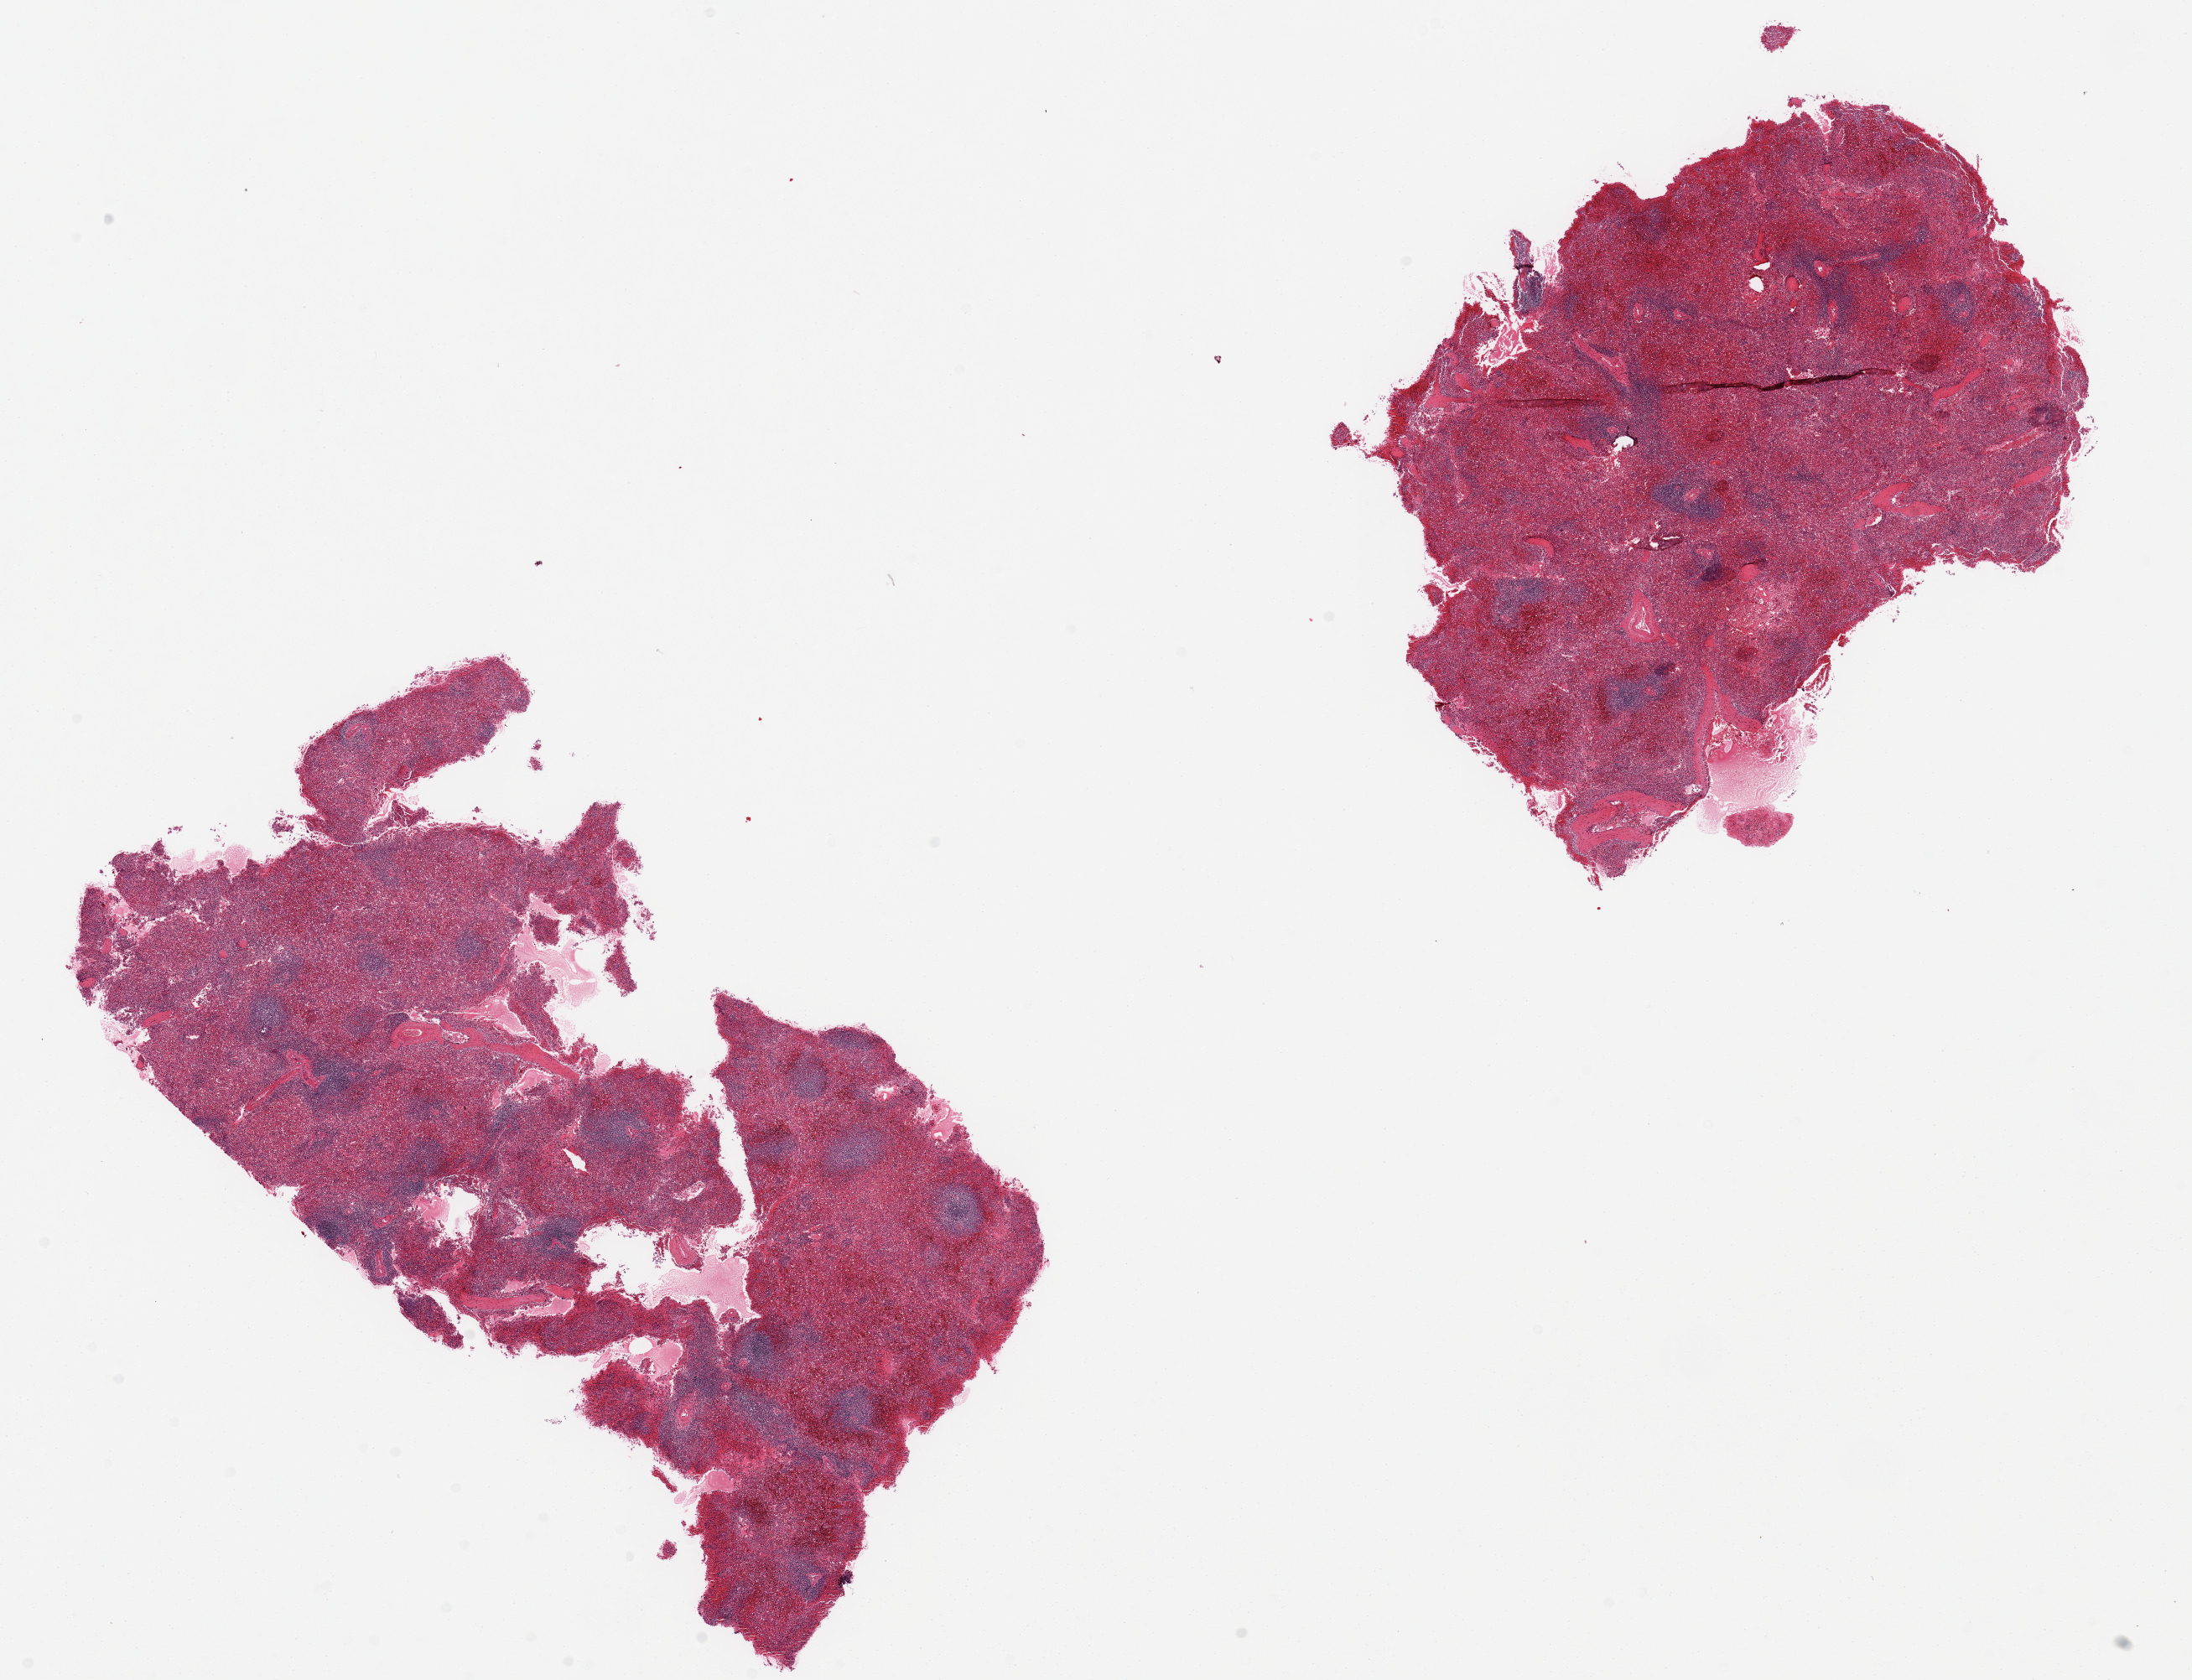
Whole-slide image, H&E stain — a low-resolution overview of the entire scanned area, about 20.7 x 15.8 mm. PAXgene-fixed, paraffin-embedded tissue. Section of spleen (target tissue). Tissue donor sample. Male donor.
* reviewer comment on this tissue sample: 2 pieces, fragmenting, moderate congestion